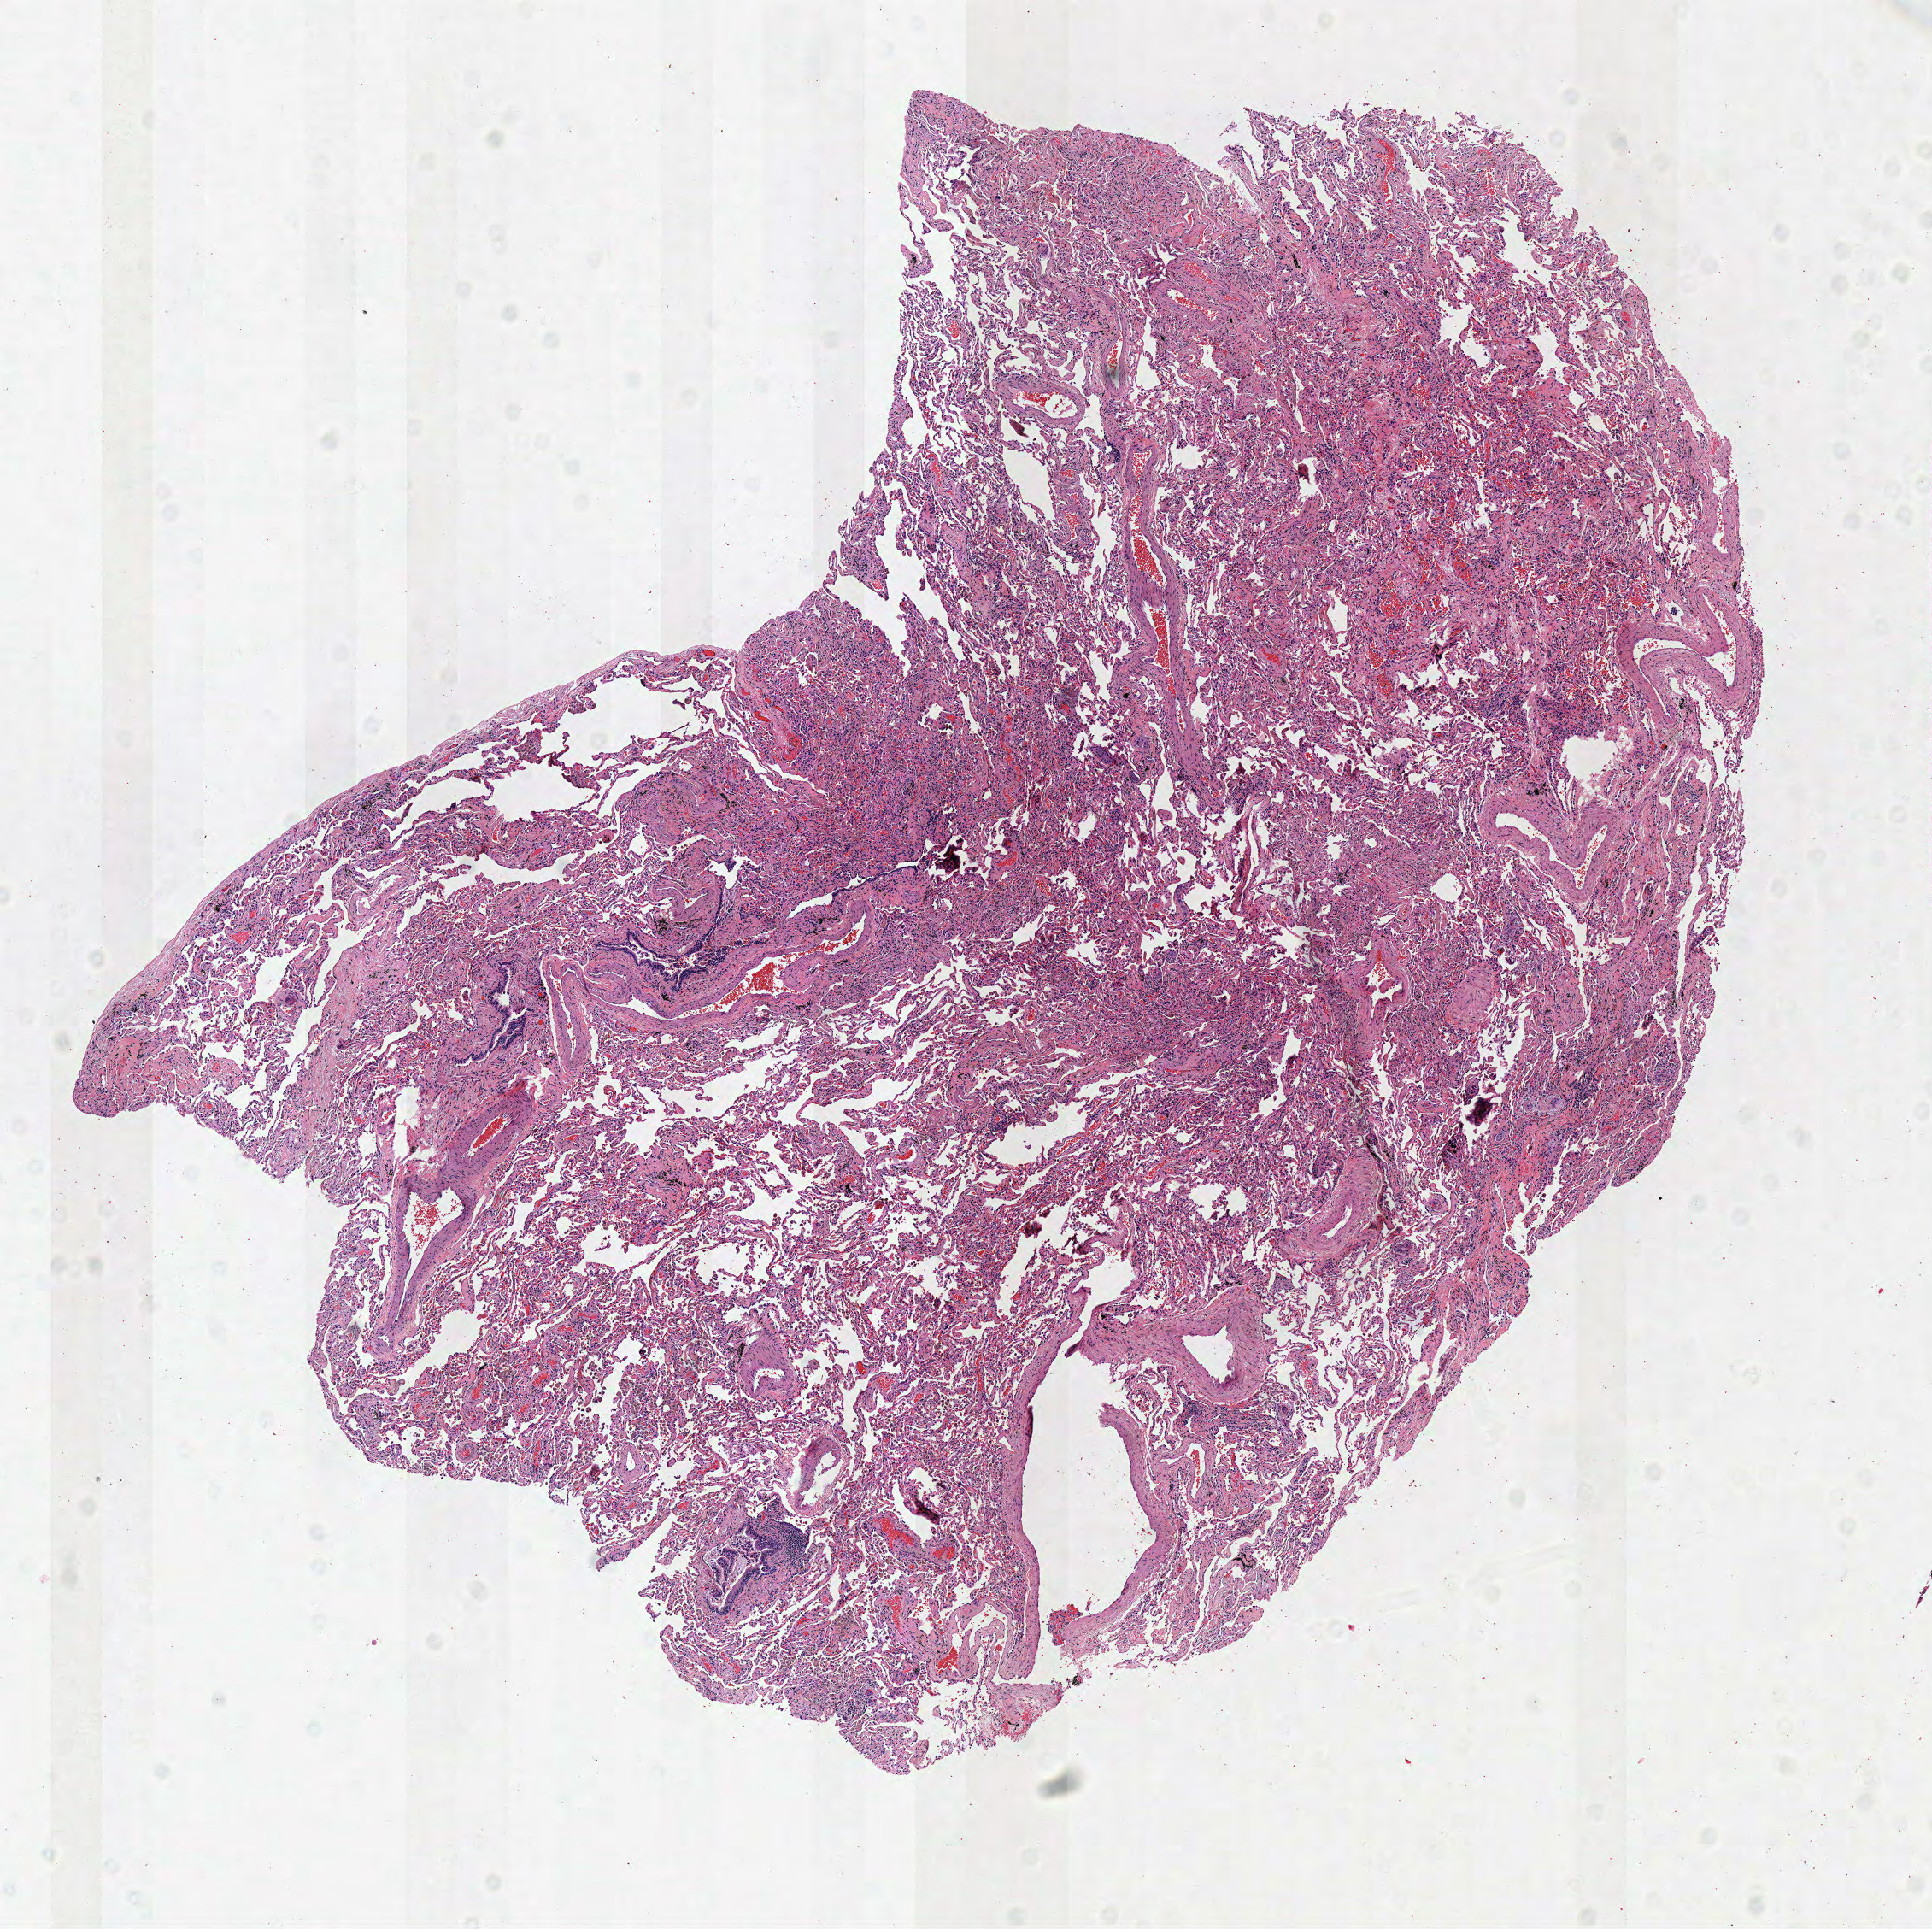
Whole-slide histology image, Hematoxylin and eosin (H&E) stained — a low-resolution overview of the entire scanned area, about 8.9 x 8.9 mm; frozen section from the top of the tissue portion; sample: solid tissue normal (non-tumour tissue), lung. Patient: female, age at initial diagnosis 65 years.
This section: solid tissue normal sample (biorepository sample class). Patient diagnosis: Adenocarcinoma, NOS (upper lobe, lung).